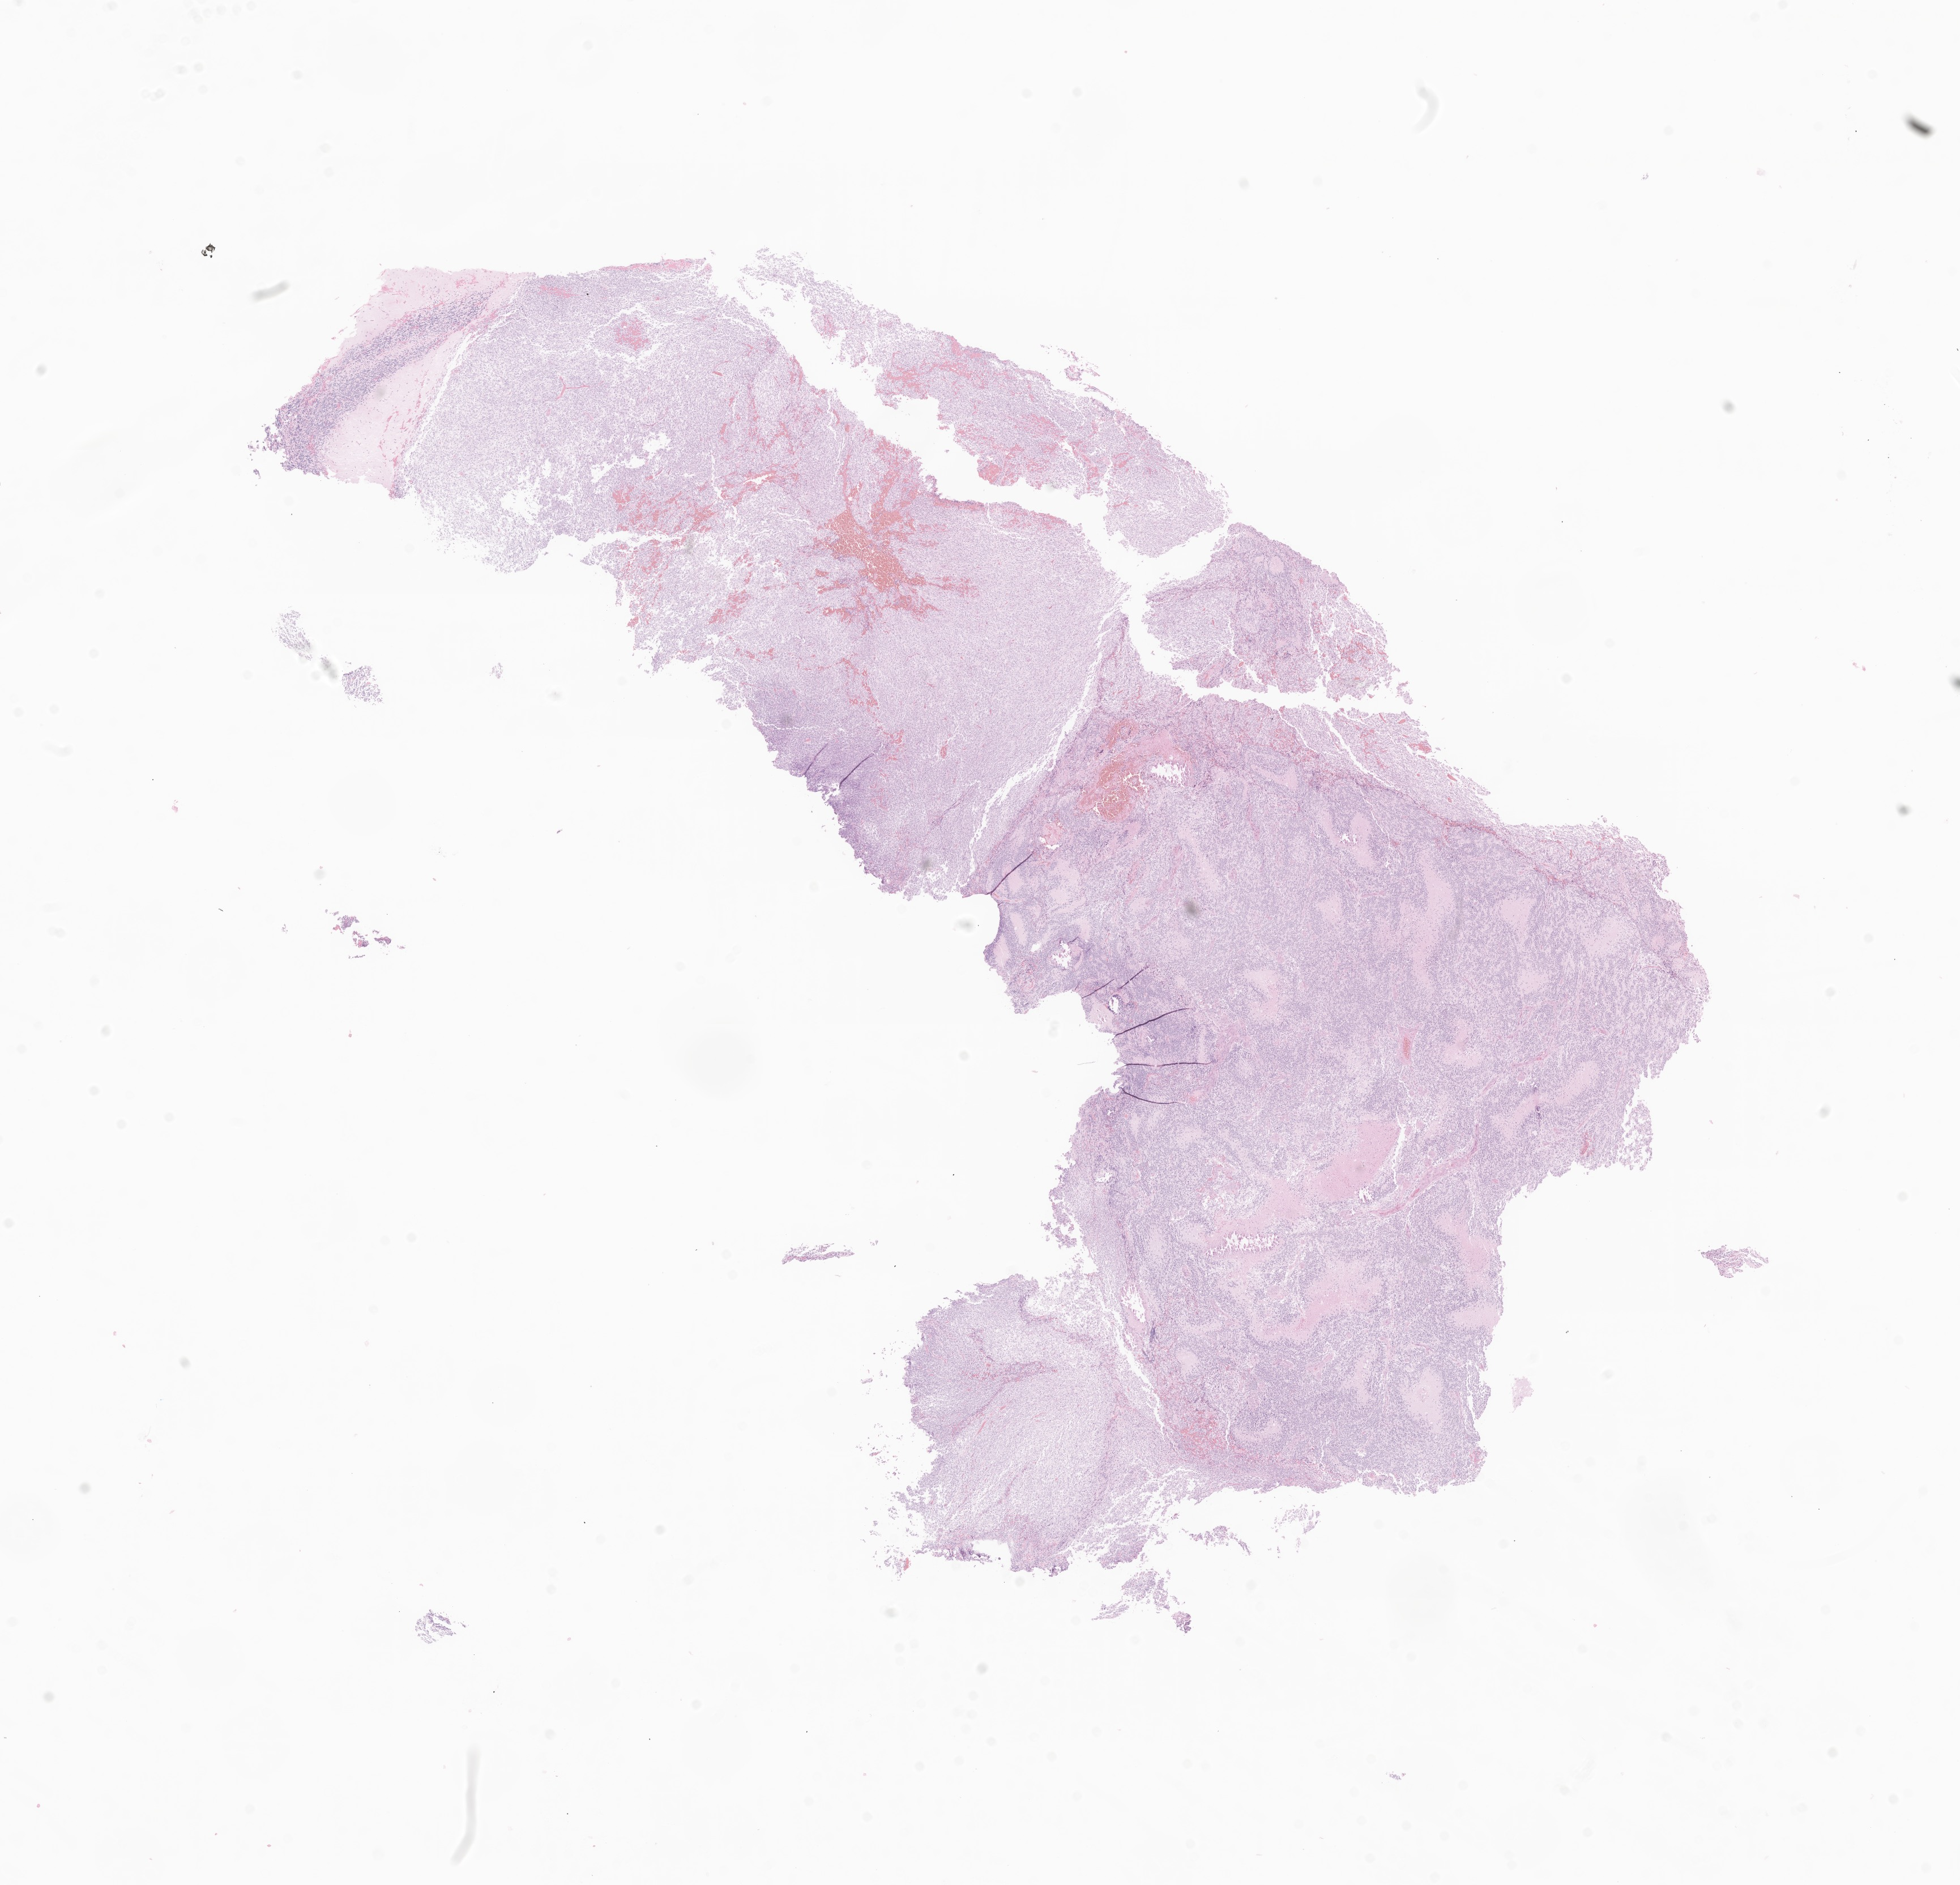
Haematoxylin and eosin whole-slide image of tumor tissue from the brain — low-resolution overview of the scanned area, about 14.6 x 14.0 mm. Formalin-fixed, paraffin-embedded (FFPE) tissue. Patient: male, age 163 months (13 years 7 months).
Diagnosis: CNS embryonal tumor, NOS.